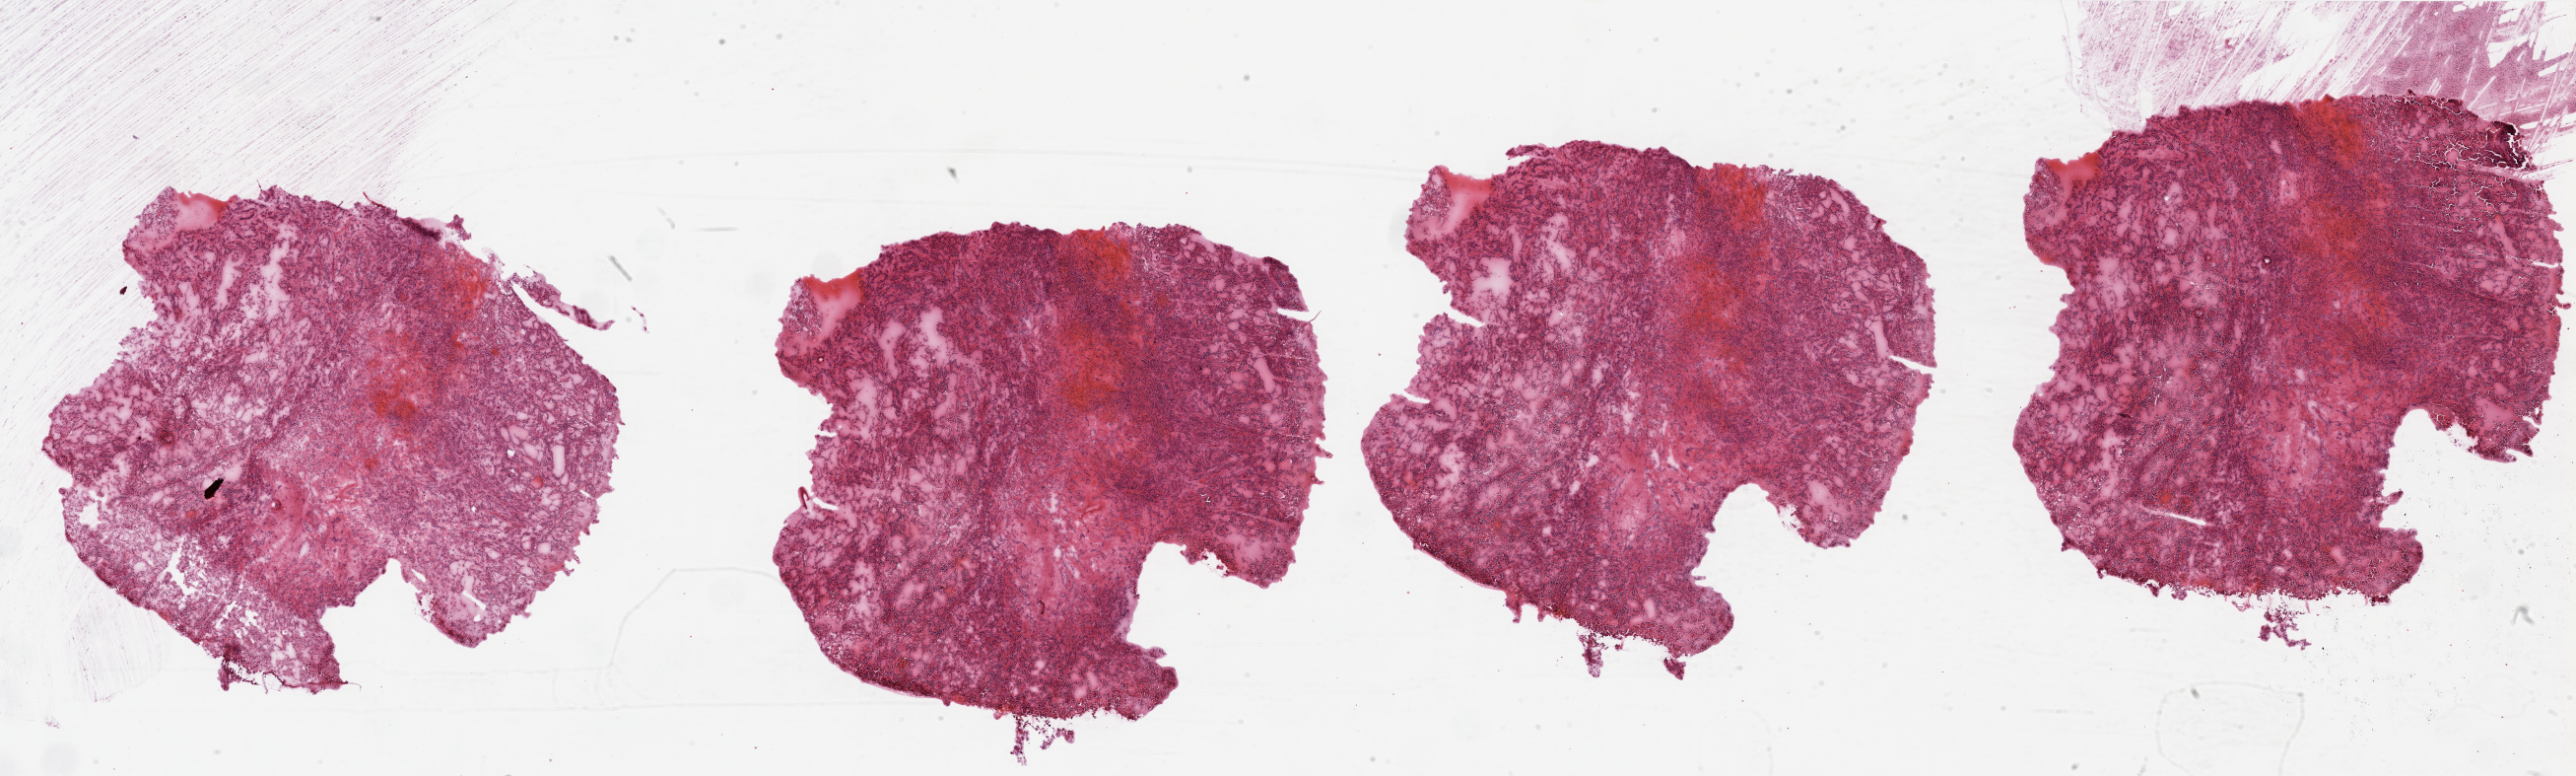
H&E whole-slide image — whole scanned area (about 41.3 x 12.4 mm, from a 20x scan) shown as a low-resolution overview. Tumour tissue sample, sampled site: kidney. 31-year-old female patient. Histologic grade: G2 (moderately differentiated). Composition of this section per pathologist review: tumour nuclei 90%, necrosis 15%.
• AJCC pathologic stage: I
• primary tumour site (as recorded): middle
• diagnosis: Renal cell carcinoma, NOS